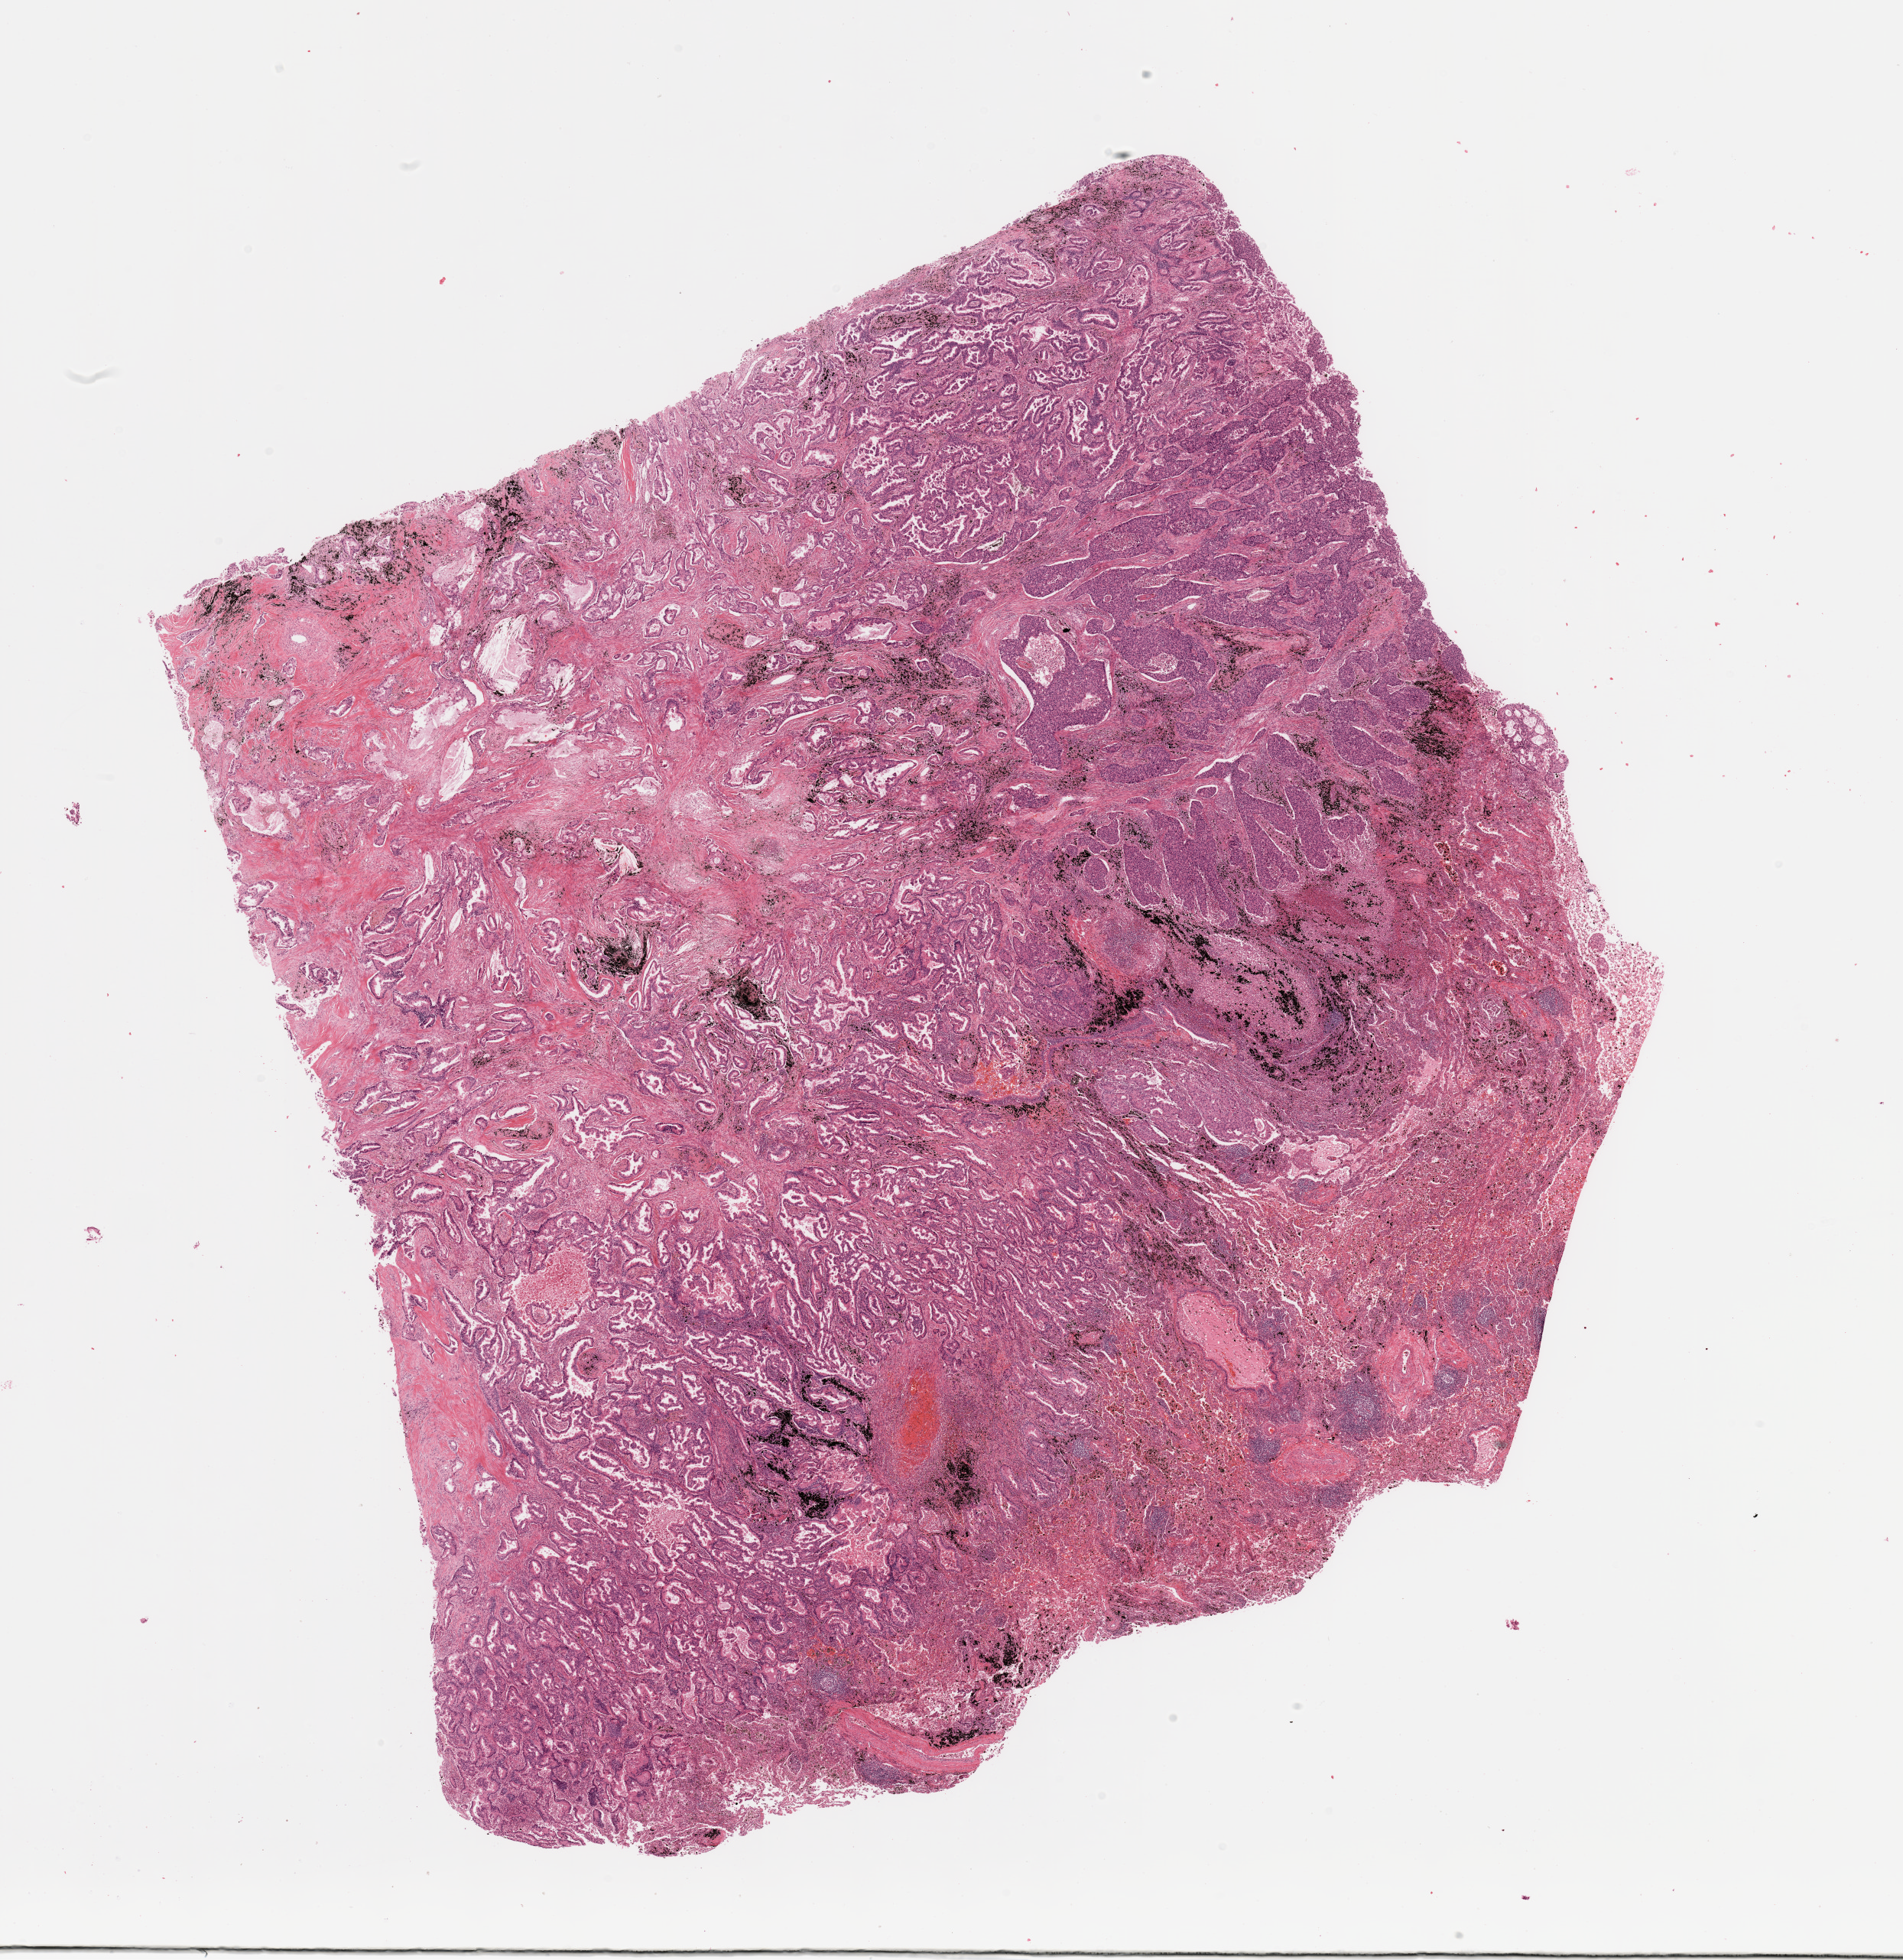
Whole-slide histology image, Hematoxylin and eosin (H&E) stained, whole scanned area (about 19.7 x 20.3 mm, slide scanned at 20x) shown as a low-resolution overview, tumour tissue sample, lung. Male, 60 y/o. Histologic grade: G2 (moderately differentiated).
• histologic diagnosis: Adenocarcinoma, NOS
• AJCC pathologic stage: IIA